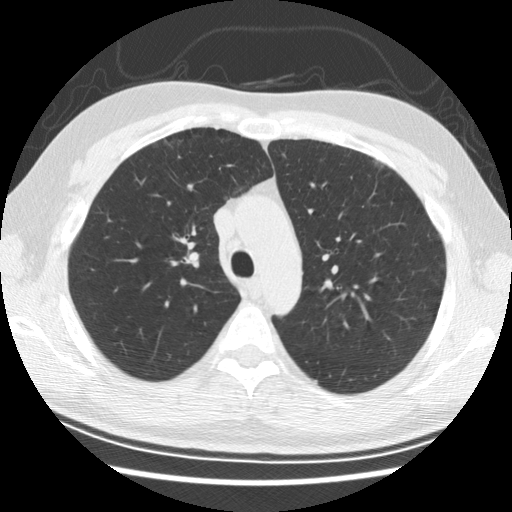
Chest CT (low-dose screening protocol), one axial image, first (baseline) screen, lung window (W 1500 / L -600 HU), 2.5 mm slice thickness. Male participant, aged 57 years at enrolment. Former smoker at enrolment.
• Expert-annotated lung lesion, bounding box [x1, y1, x2, y2] px = [162, 221, 219, 284].
• The screening reader recorded 6 non-calcified nodules or masses ≥4 mm on this exam; which of them this box marks is not recorded.
• Official screen result: negative screen, minor abnormalities not suspicious for lung cancer.
• Lung cancer was diagnosed 766 days after this screen (after the second annual screen): adenocarcinoma, NOS, right upper lobe, poorly differentiated (G3), stage IB (AJCC 6th edition), 25 mm at pathology.